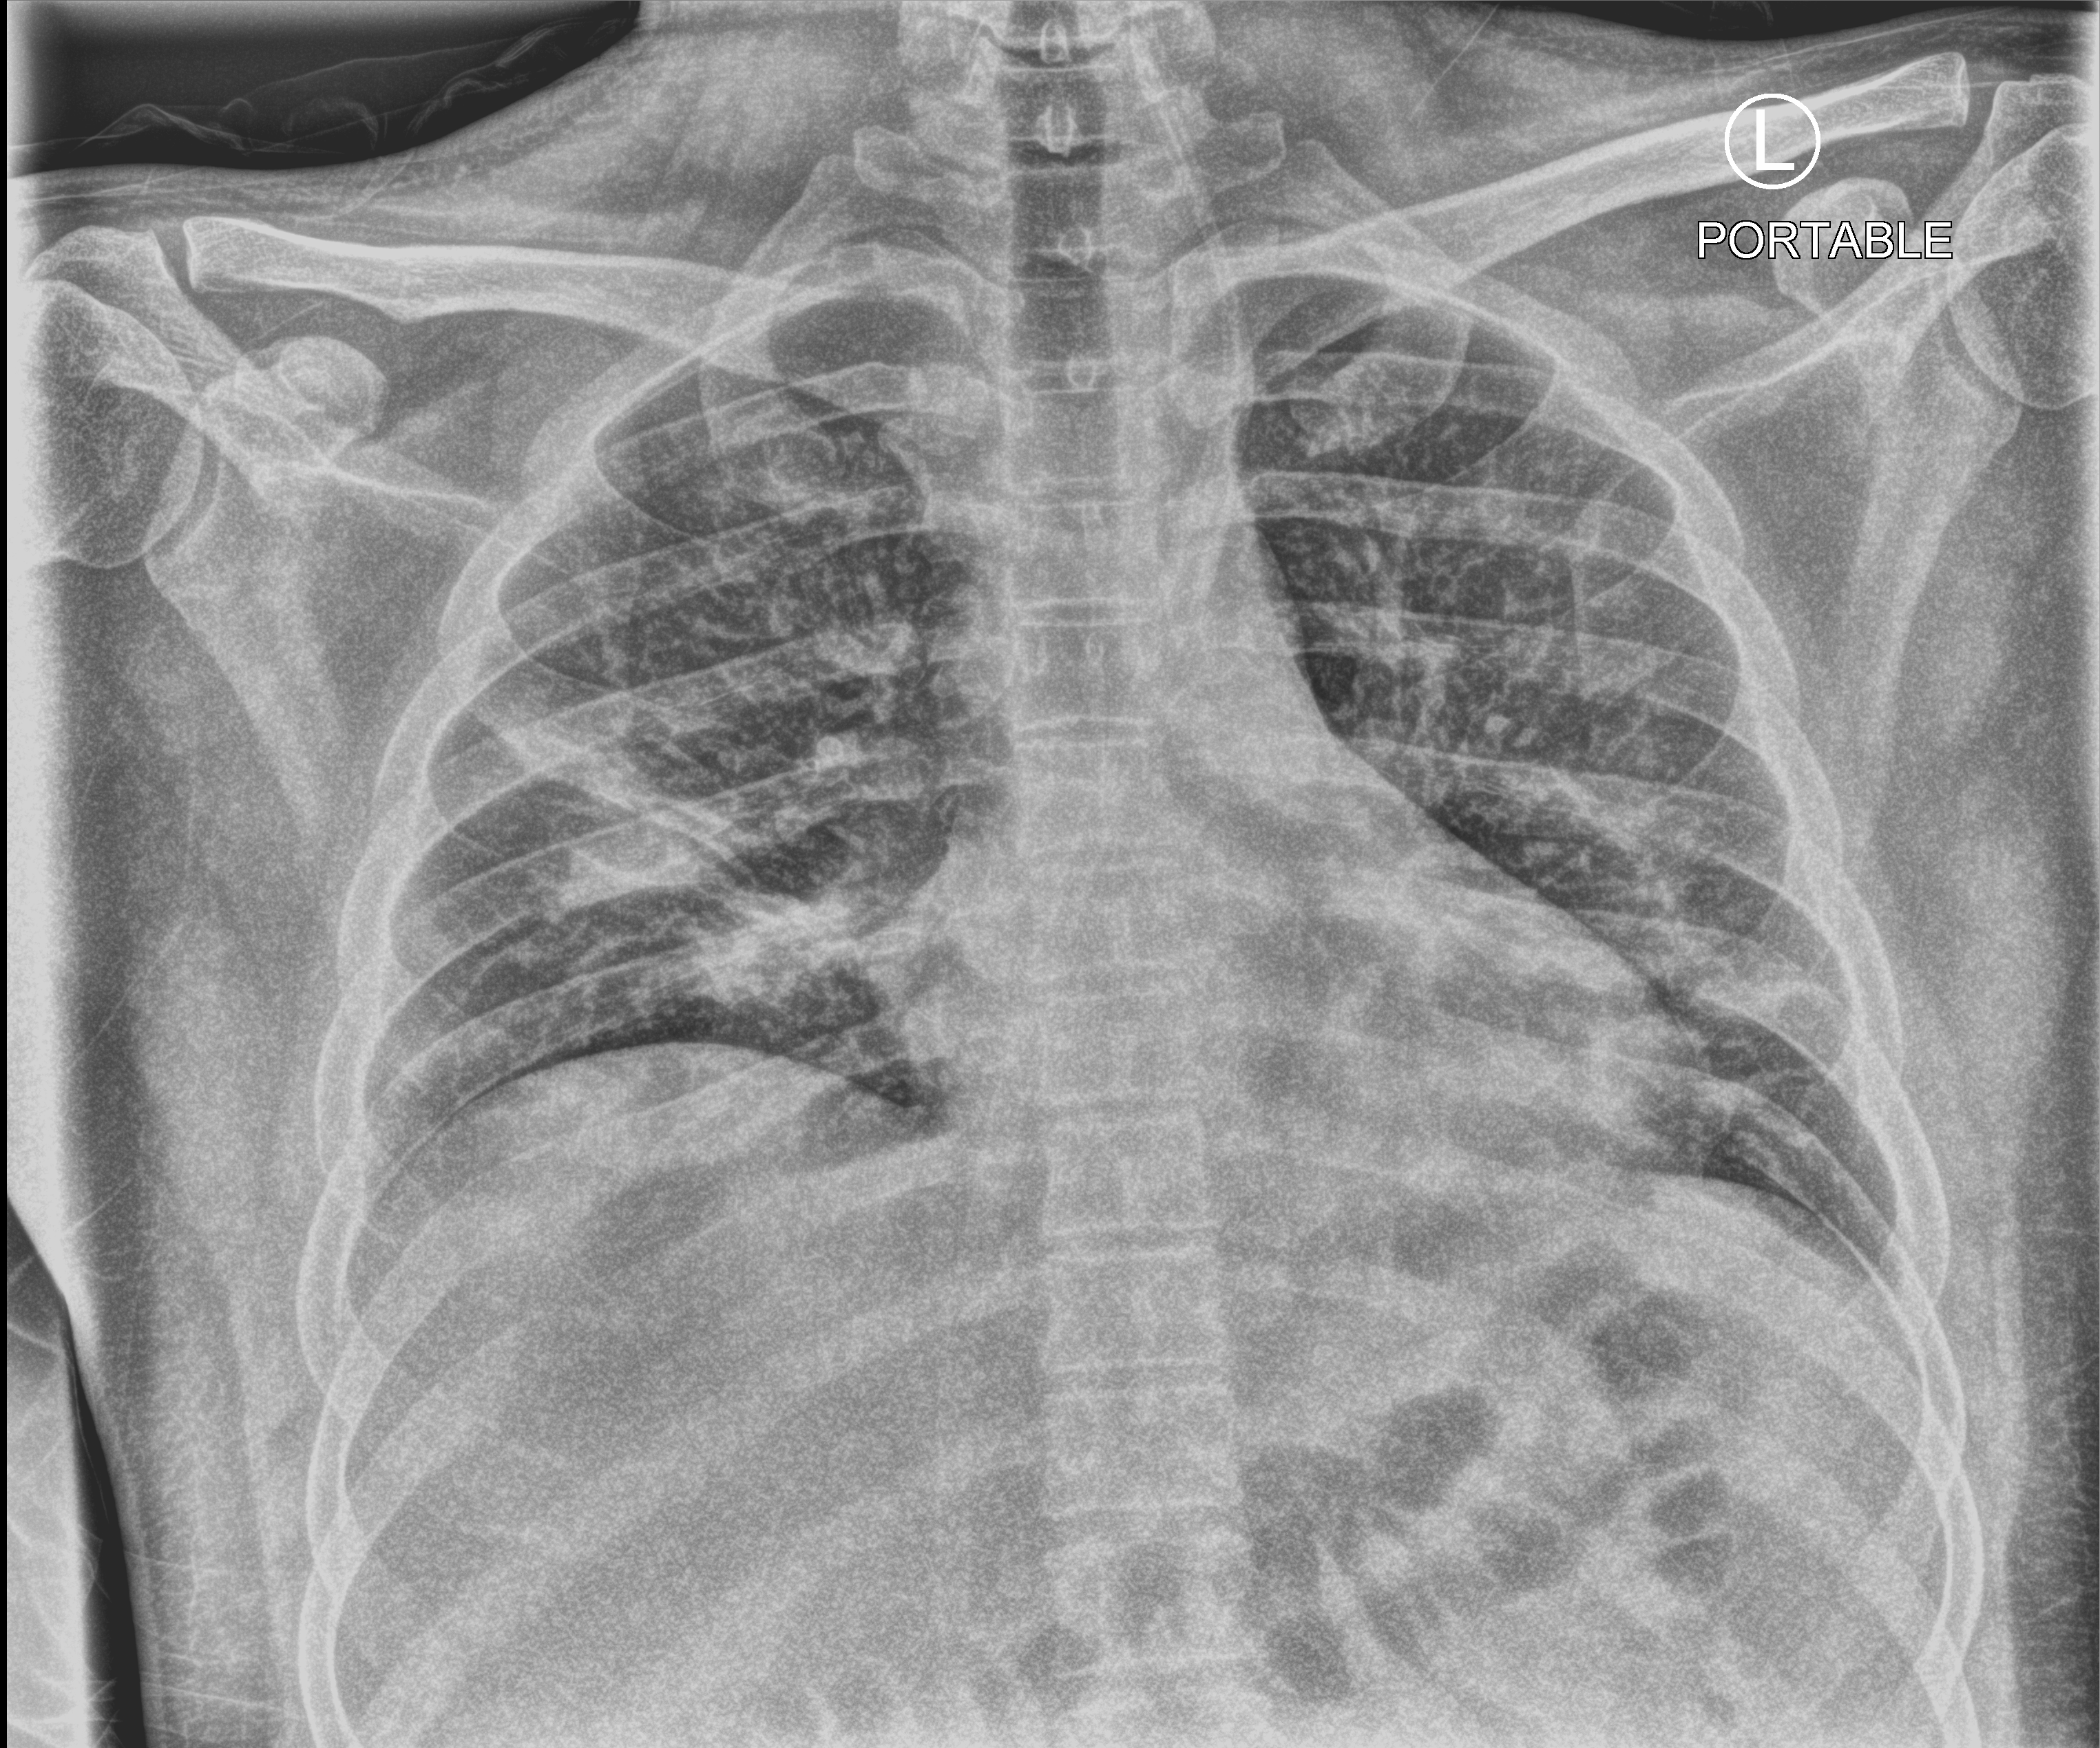
Bedside chest radiograph (computed radiography), anteroposterior (AP) projection. Male patient hospitalised with COVID-19, age 18–59 years.
From the hospital-stay record, not from the radiograph (when in the stay this image was taken is not recorded):
- mechanically ventilated during this hospital stay: no
- chronic kidney disease (admission record): no
- other chronic lung disease (admission record): no